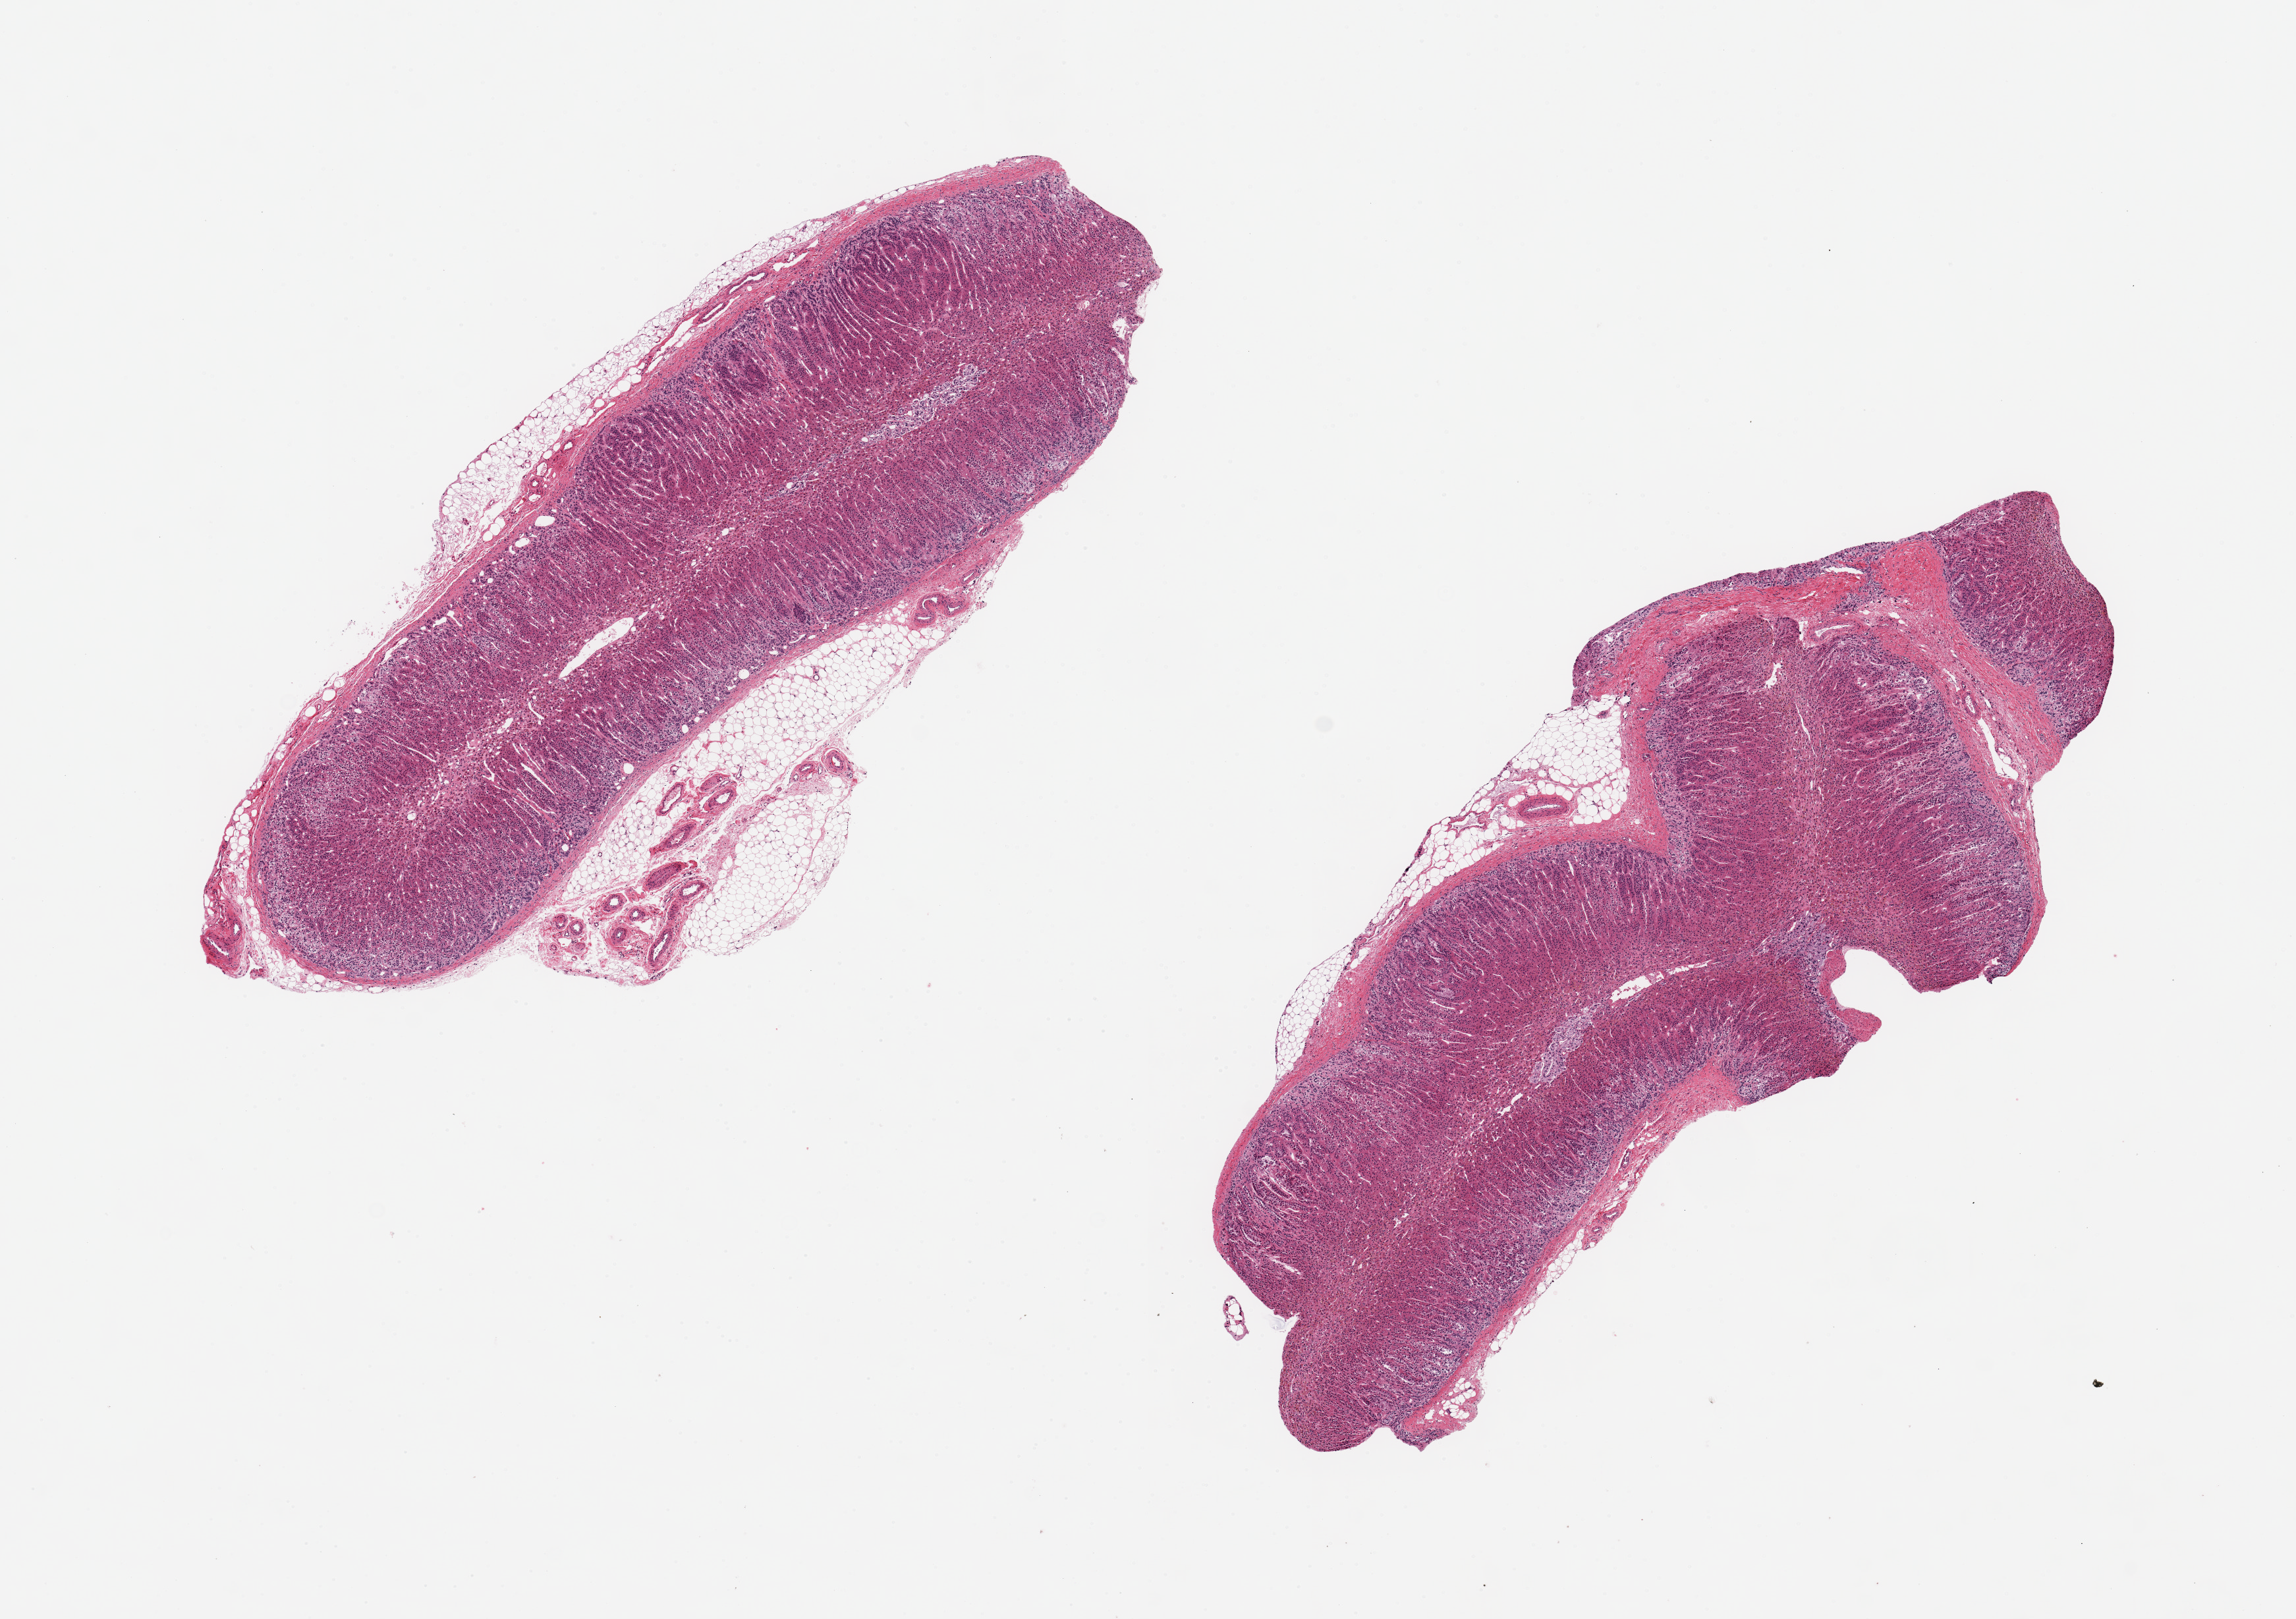
Digitized hematoxylin and eosin (H&E)-stained section — shown as a low-resolution overview of the whole scanned area (about 13.8 x 9.7 mm), PAXgene-fixed paraffin-embedded (PFPE) section, target tissue: adrenal gland, tissue donor sample. Female donor.
- review note (as recorded): 2 pieces, ~7x2 mm; ~10% adipose; very small medulla